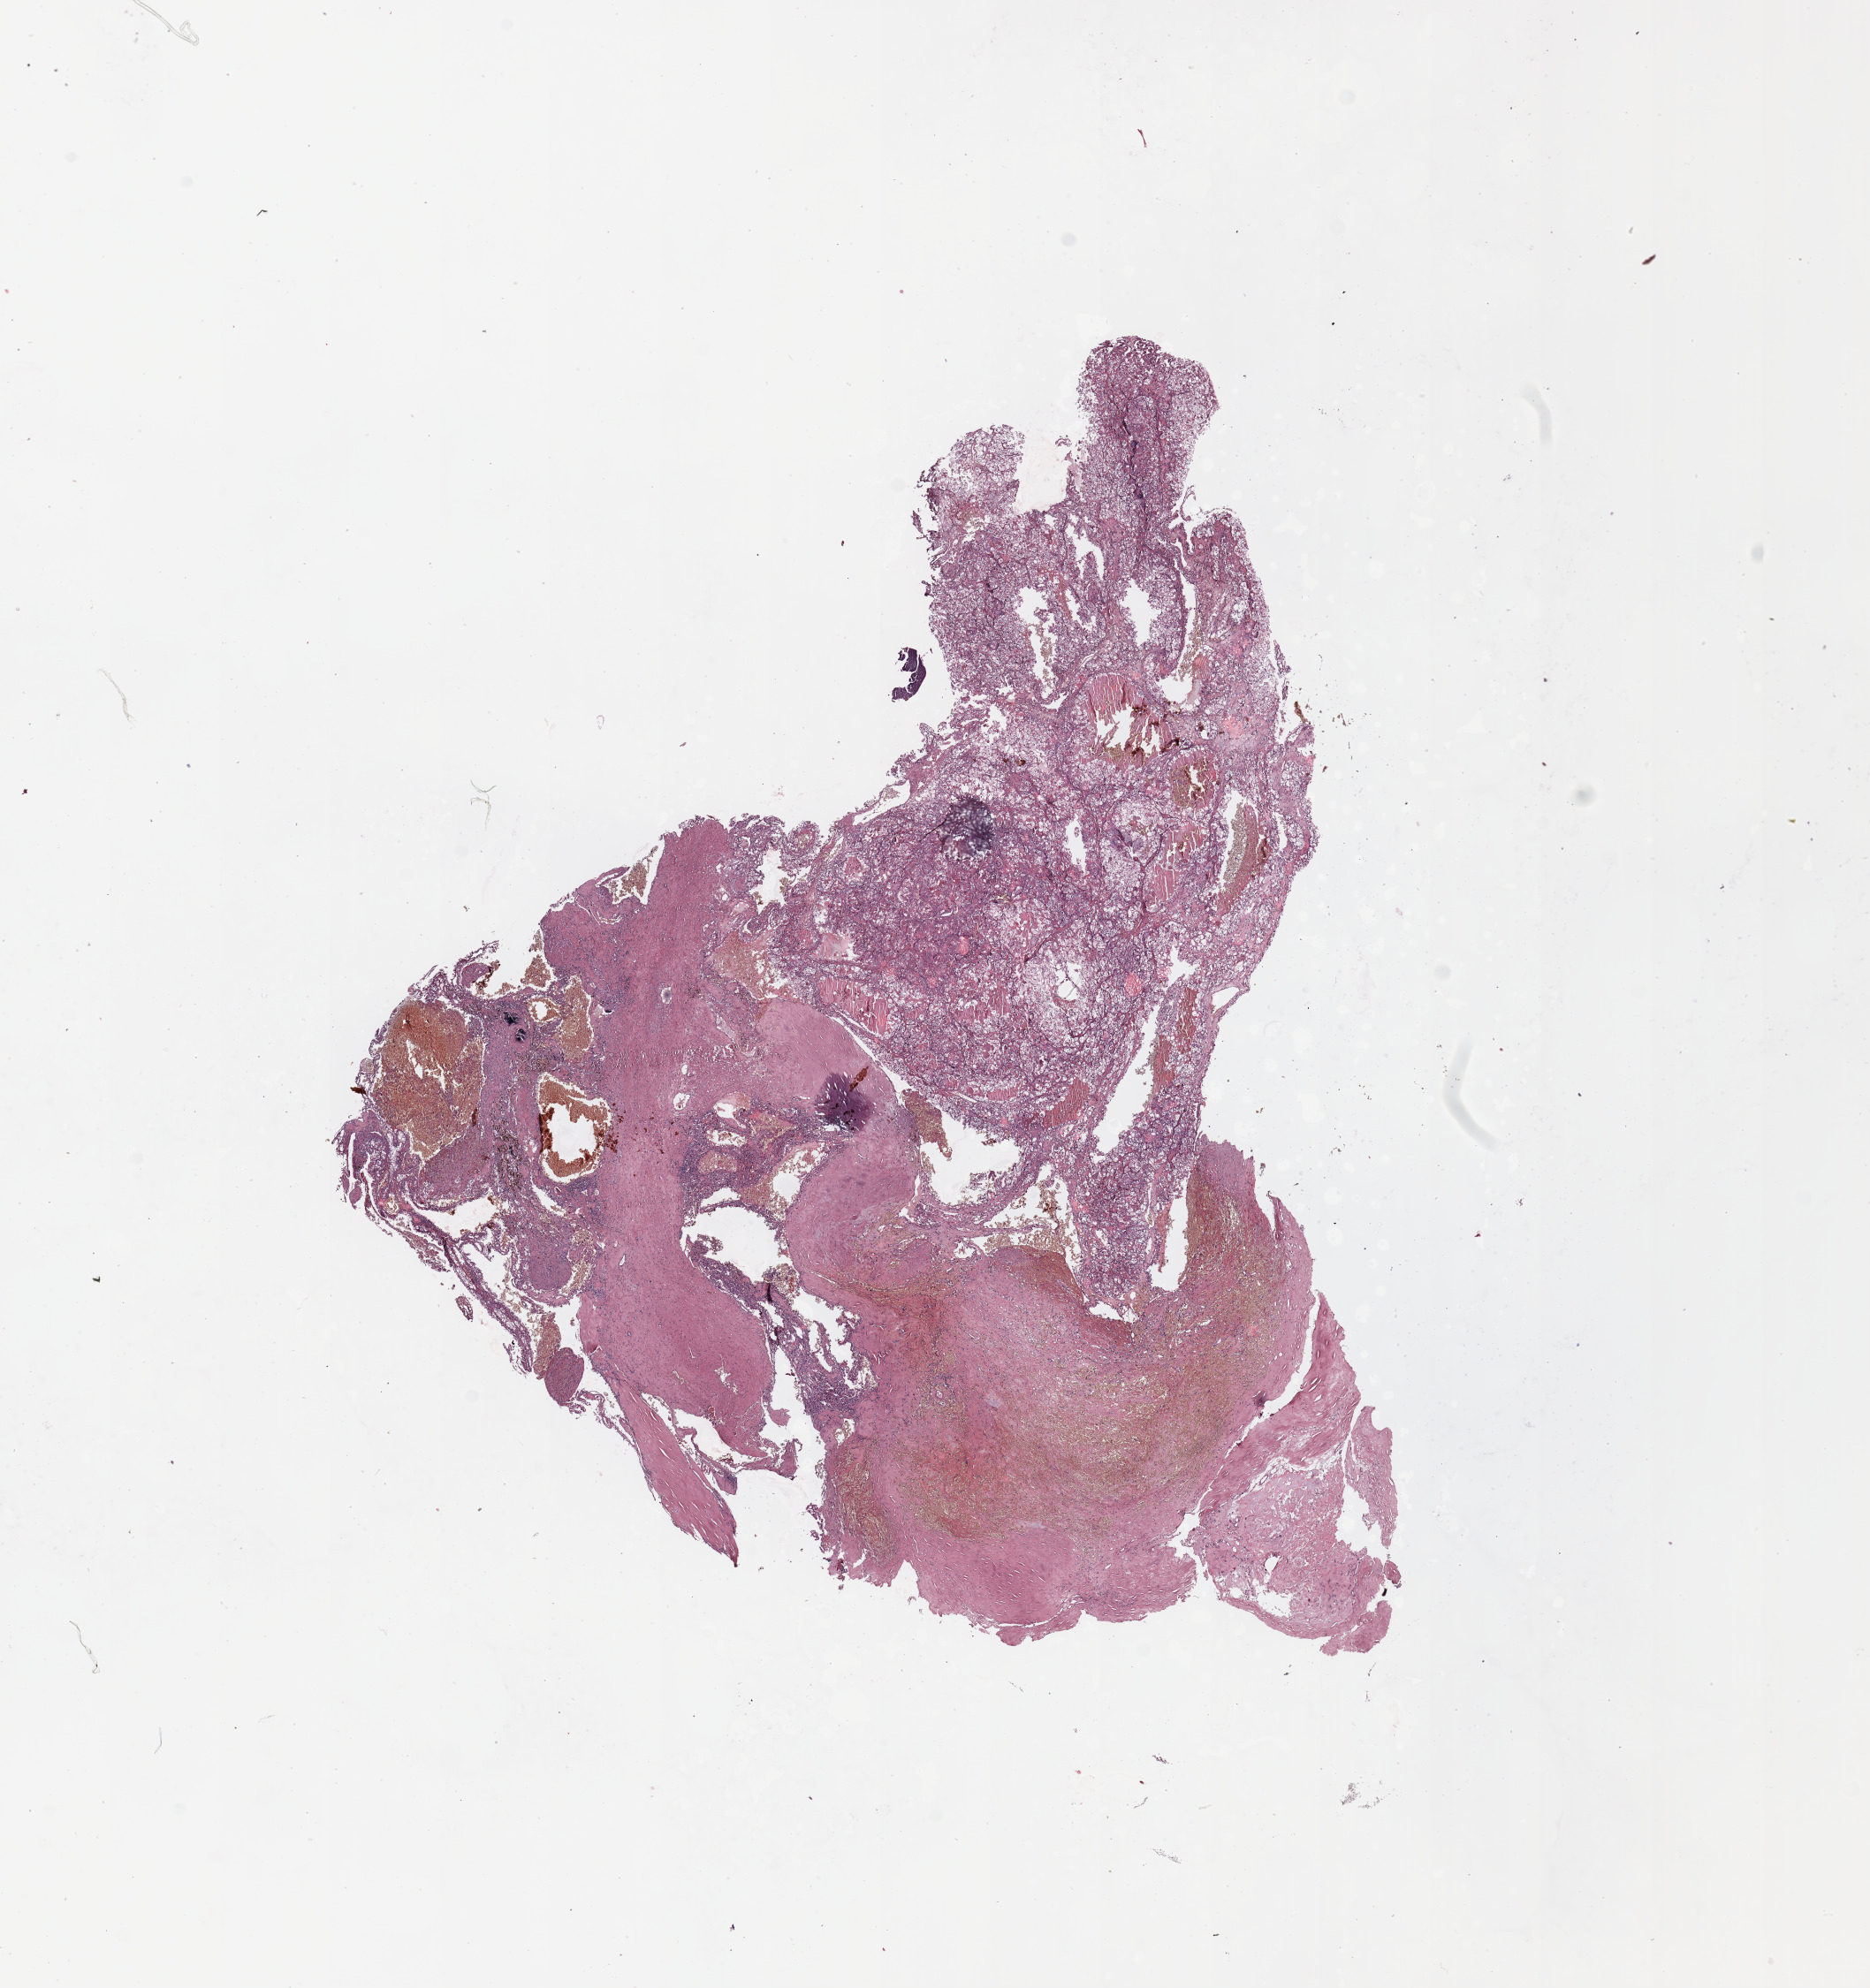
Whole-slide histology image, Hematoxylin and eosin (H&E) stained, low-resolution overview of the scanned area, about 16.7 x 17.8 mm (from a 20x scan), tumour tissue sample, sampled site: kidney. Patient: male, age 60 years. Histologic grade: G2 (moderately differentiated). Pathologist review of this section (percent, as recorded): tumour nuclei 80%, necrosis 15%.
• primary tumour site (as recorded): upper pole
• AJCC pathologic stage: II
• histologic diagnosis: Renal cell carcinoma, NOS